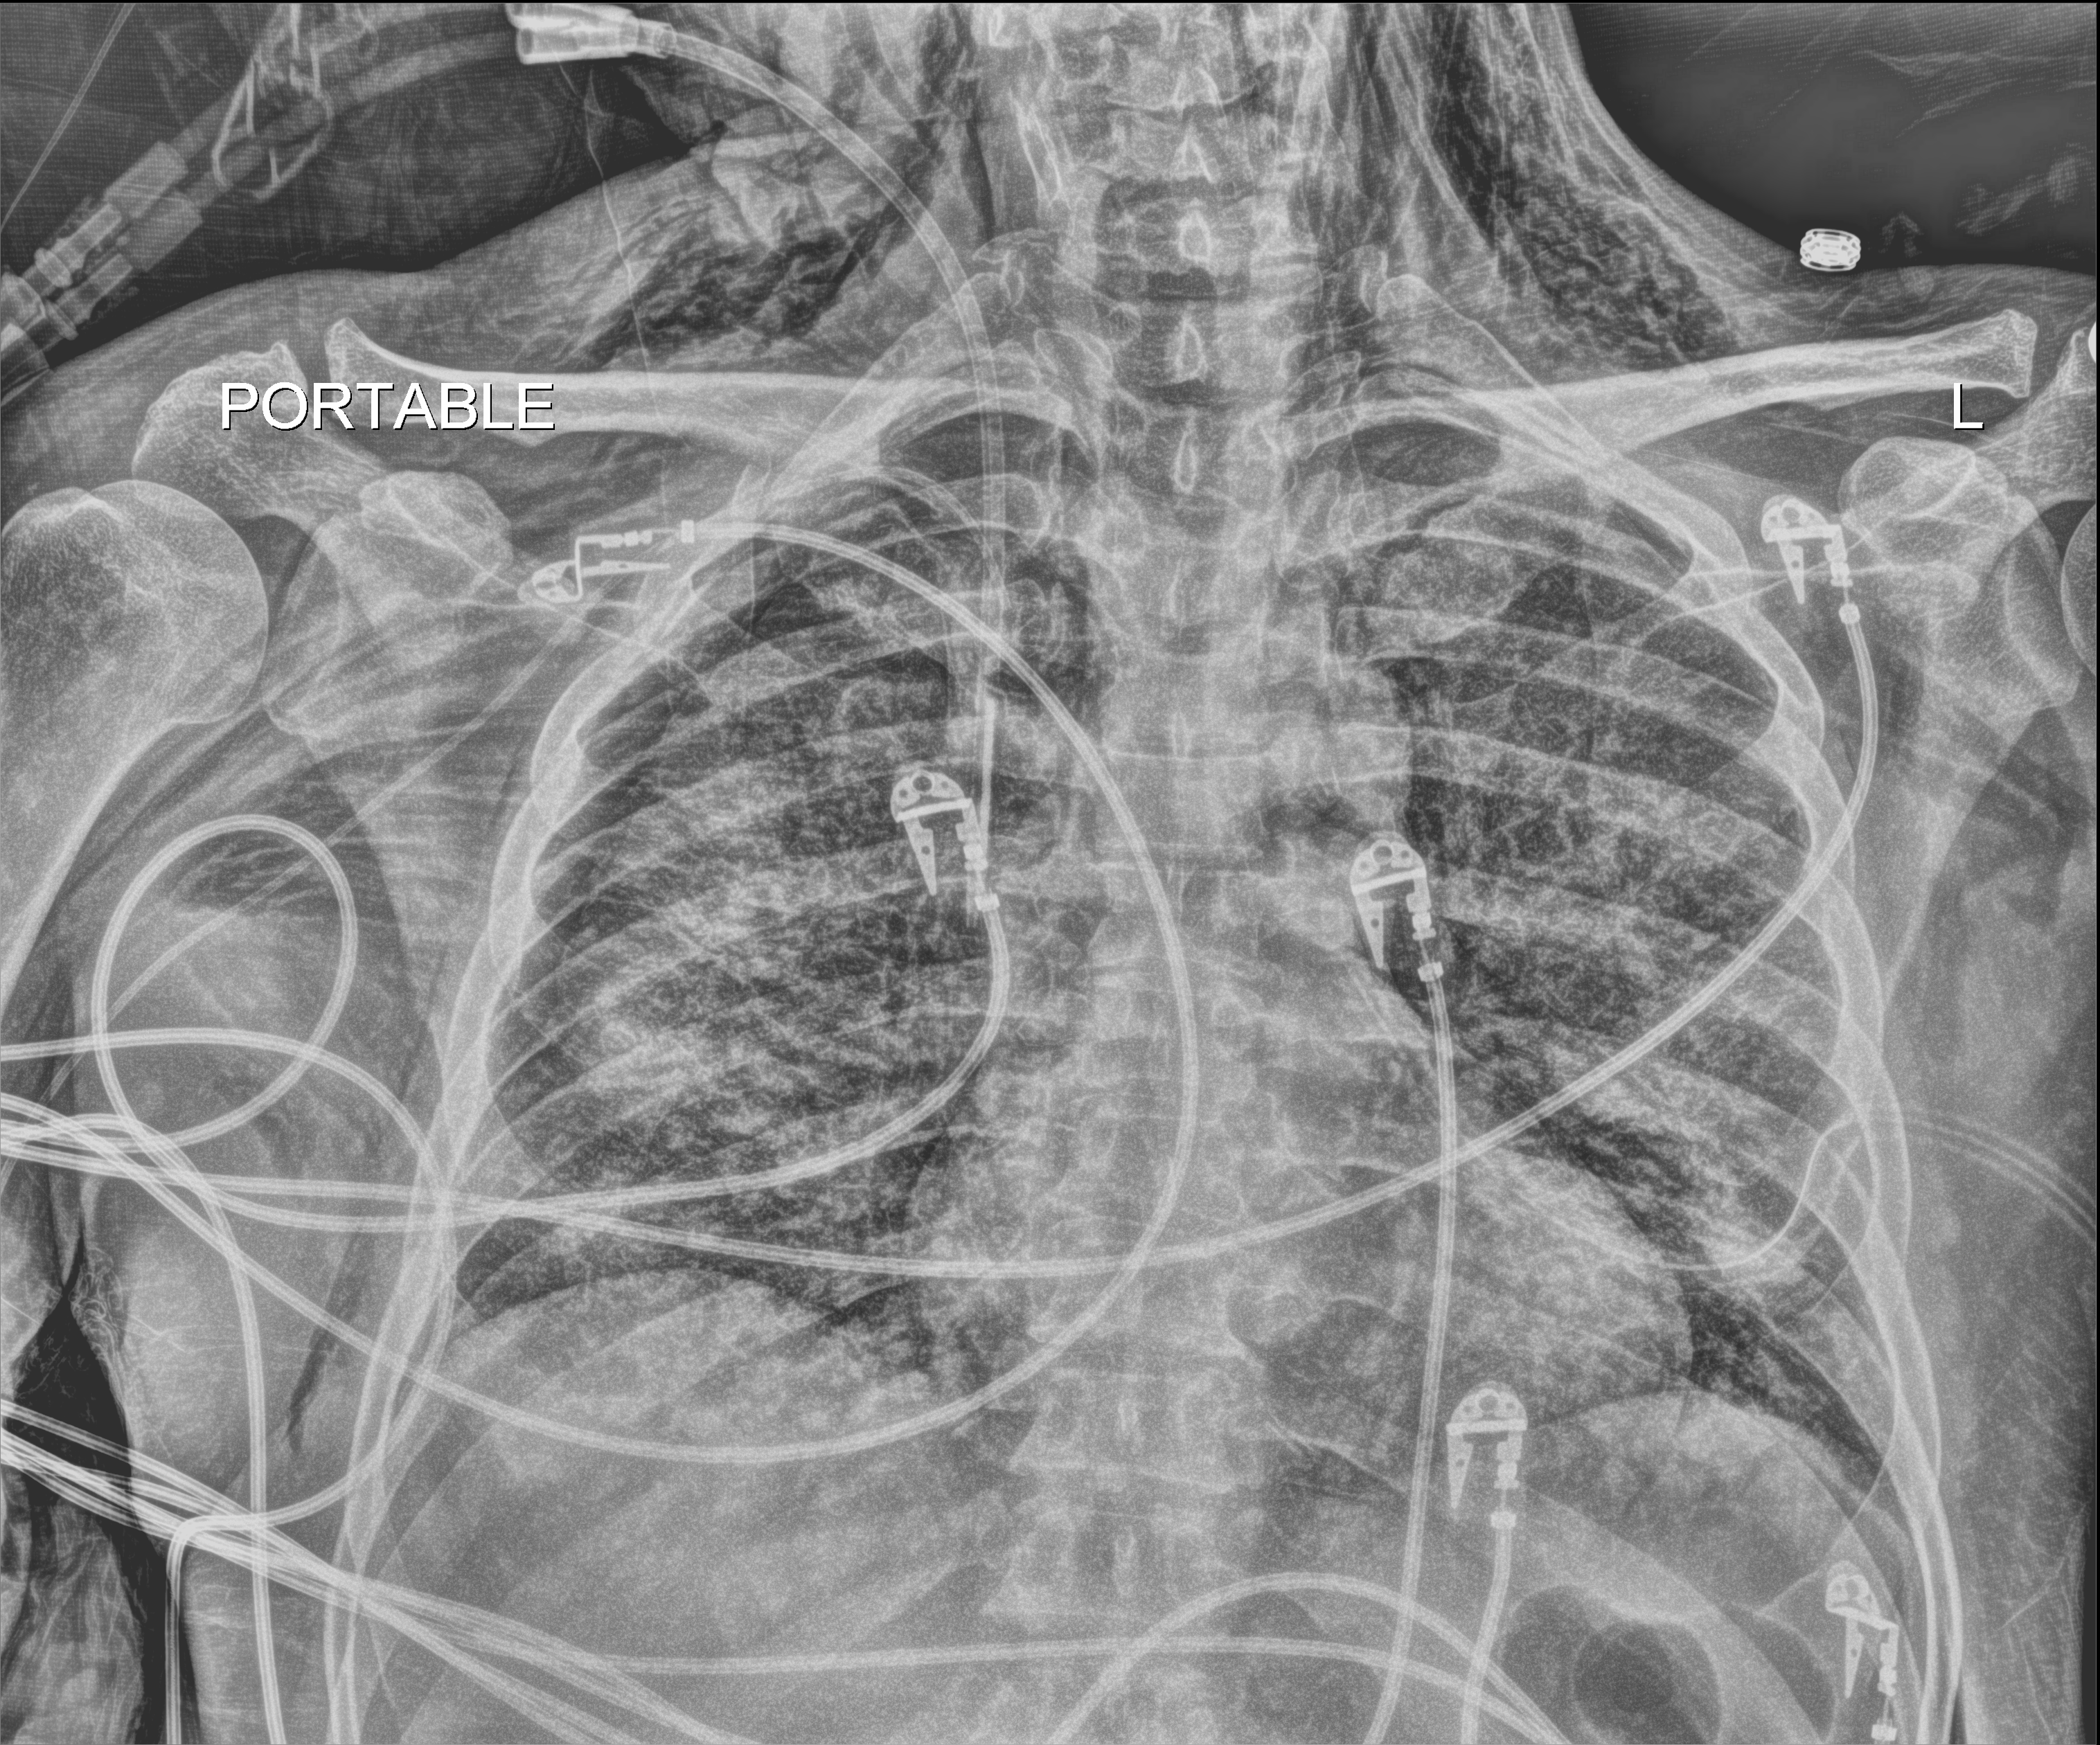
Chest radiograph (digital radiography), anteroposterior (AP) projection. Male patient hospitalised with COVID-19, age 18–59 years.
Admission-level facts for this patient (not findings on this image; timing relative to this image not recorded): hypertension (admission record): no.